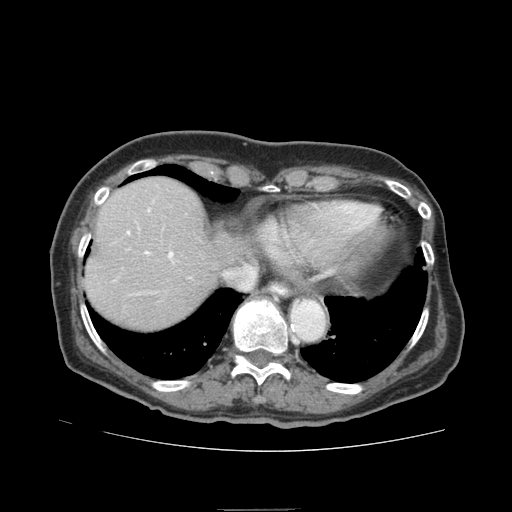
Contrast-enhanced abdominal CT (liver protocol), one axial slice; slice 70 of 95 in the series (ordered by position); soft-tissue window (W 400 / L 40 HU); 512 × 512 image matrix. Case-level facts recorded for this patient, not image findings: diagnosis: hepatocellular carcinoma (patient treated with transarterial chemoembolisation; whether this scan precedes or follows treatment is not stated here); TNM stage (as recorded): Stage-IVA; Child-Pugh class: B.
Outlined on this slice (semi-automatically segmented with operator editing):
- liver parenchyma outside the tumour (the mass and vessels are separate outlines, so this box may not span the whole liver): box from (x=84, y=177) to (x=244, y=328) px
- liver vessels: (x=127, y=208)–(x=174, y=262)